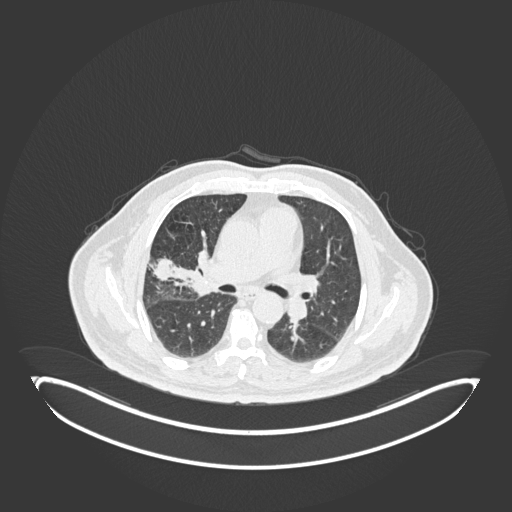
Chest CT, one axial slice. 120 kVp. Lung window (W 1500 / L -600 HU). 1 mm slice thickness. 512 × 512 image matrix, field of view 500 × 500 mm. Male patient, age 72 years. Case-level facts recorded for this patient, not image findings: clinical TNM (as recorded): T1c N0 M0; histopathological grade: G2.
Outlined on this slice (rectangle marked by the reading radiologist):
- lung tumour (recorded histology: squamous cell carcinoma): bounding box (x1, y1, x2, y2) in pixels: (183, 247, 219, 300)